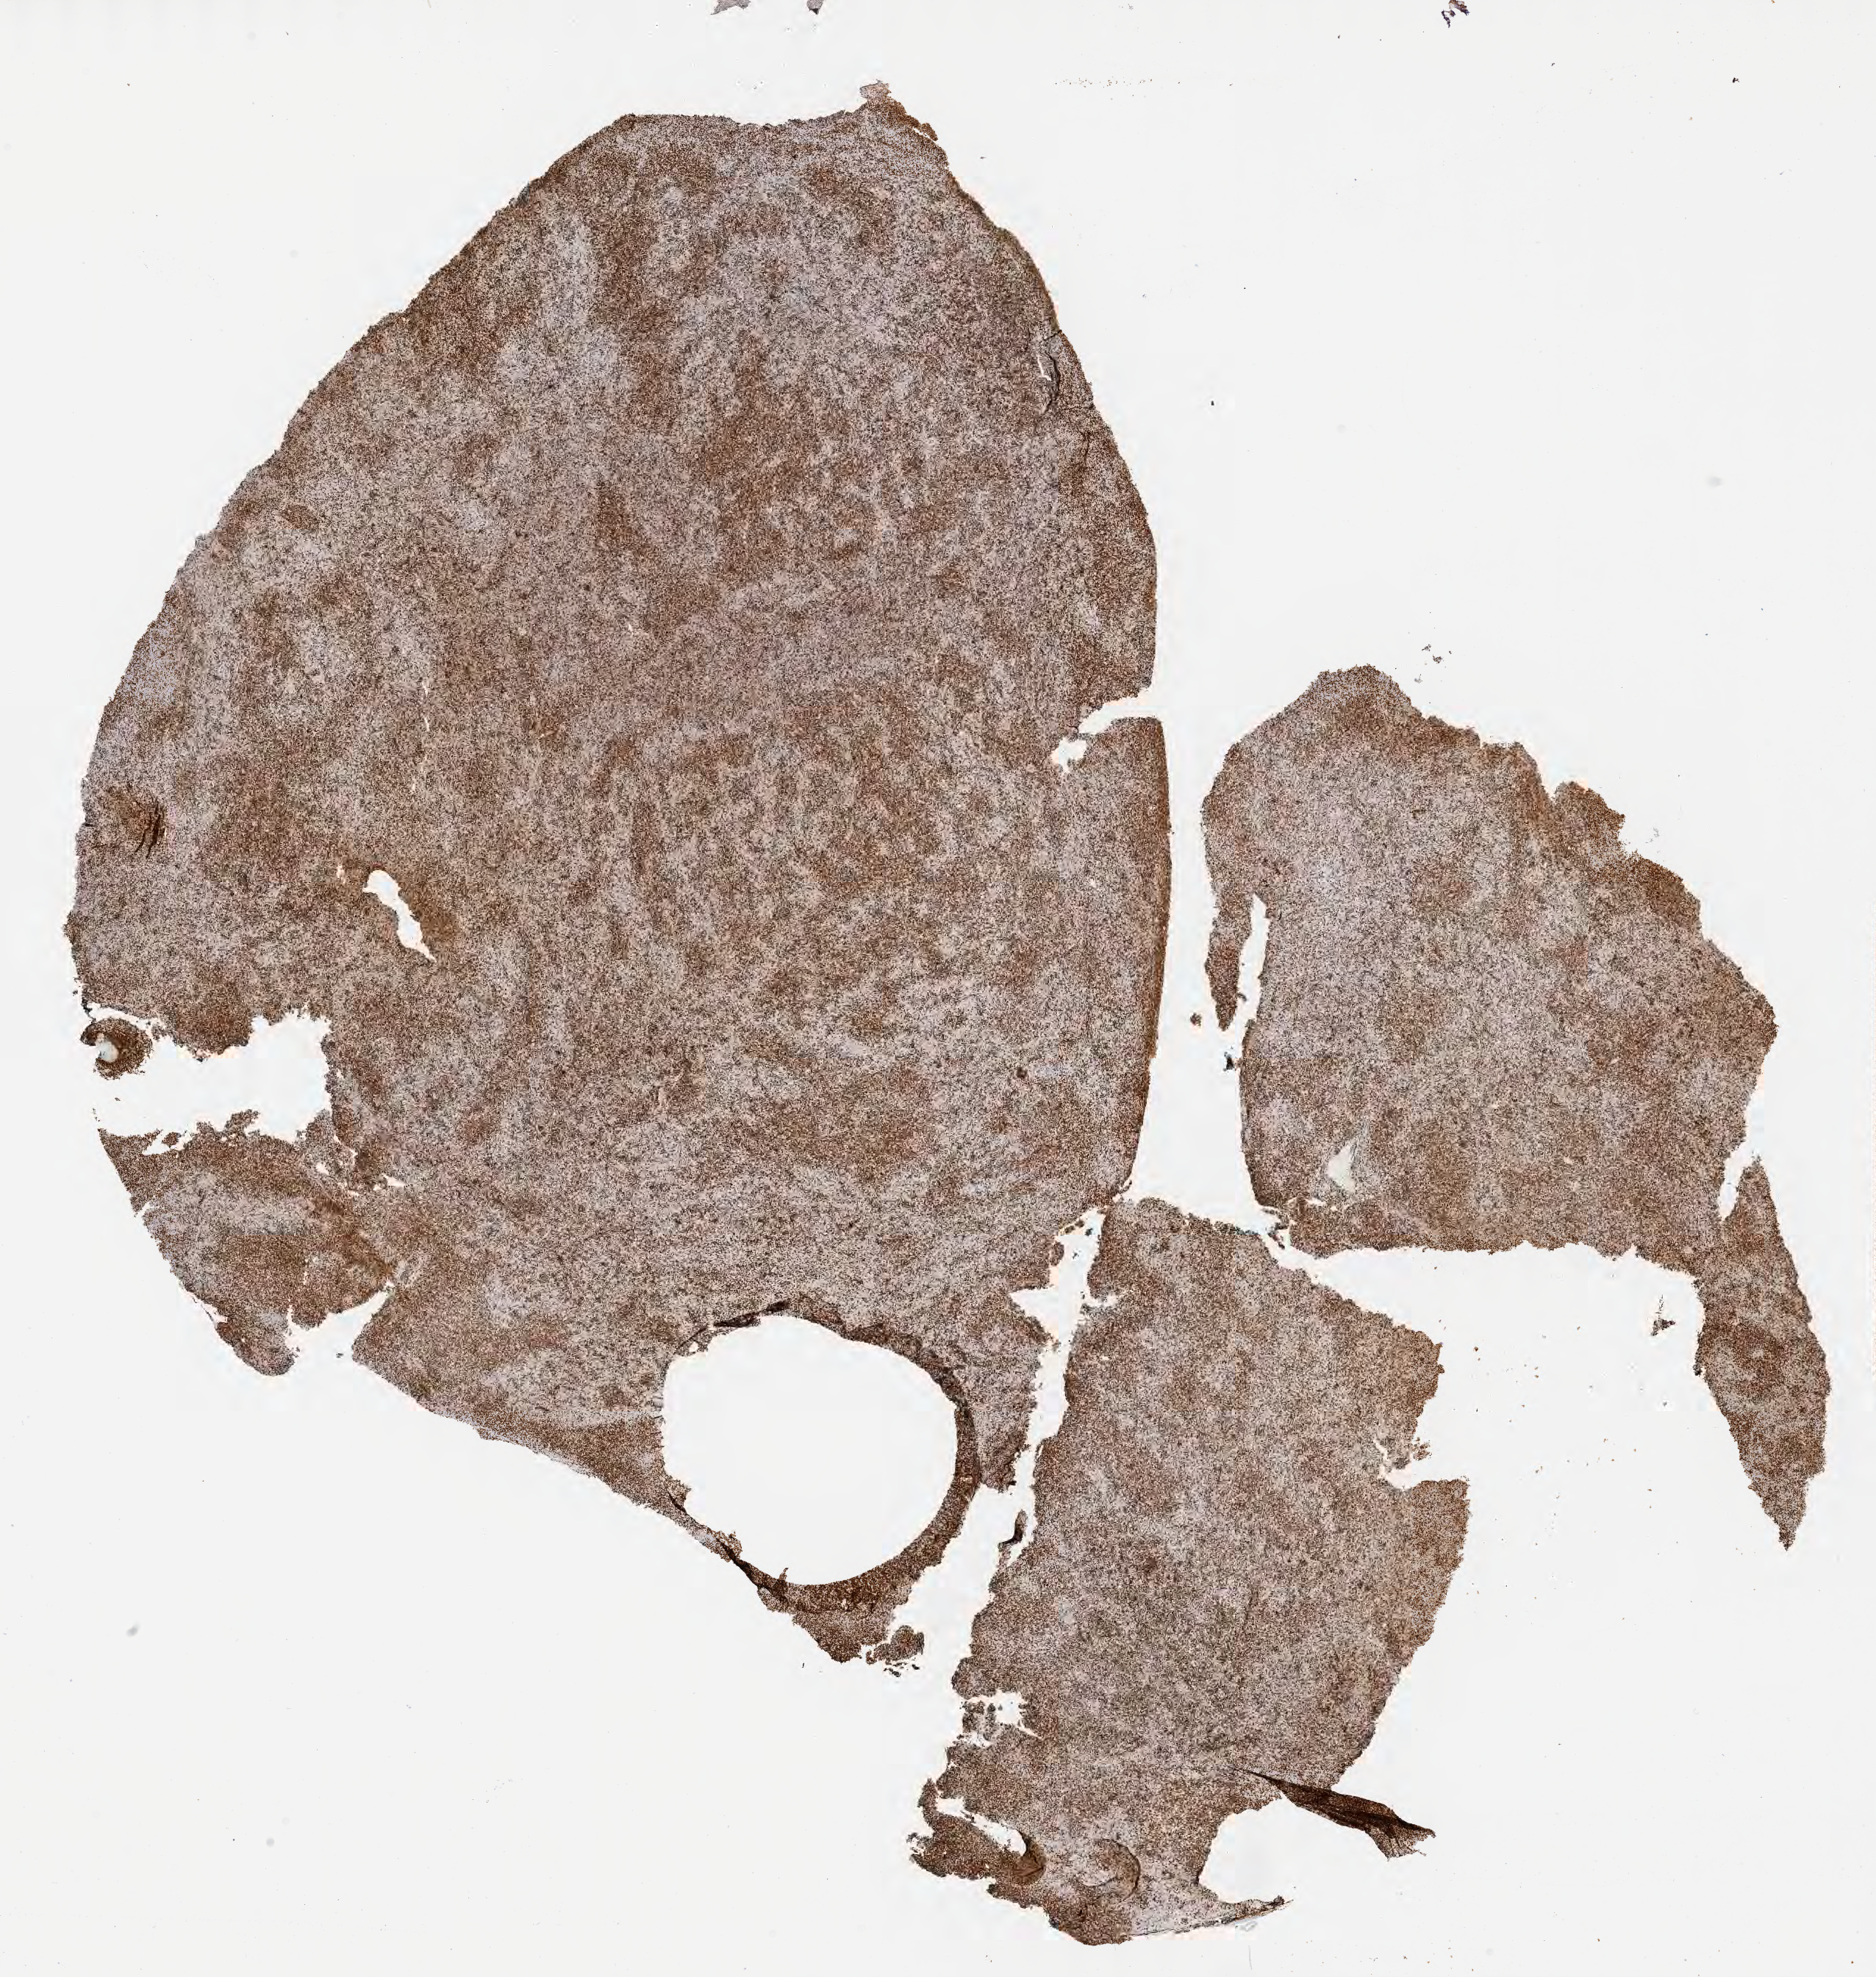
IHC for CD3, whole-slide image, a low-resolution overview of the entire scanned area, about 20.6 x 21.7 mm, tumor tissue, site: liver. Female patient, aged 46.
Histologic diagnosis: Diffuse large B-cell lymphoma, NOS.